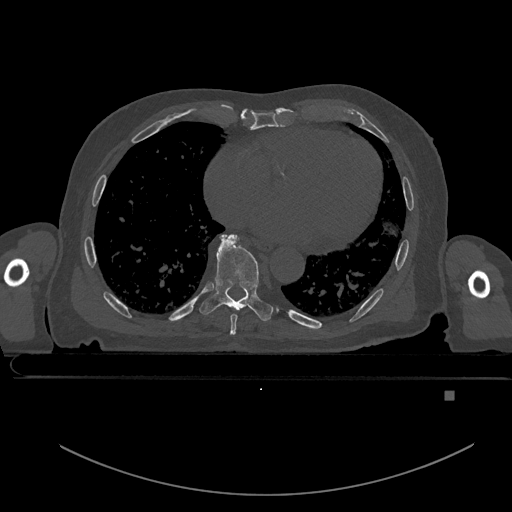
CT including the spine, one axial slice. Bone window (W 1800 / L 400 HU). 0.5 mm slice thickness. 512 × 512 image matrix, field of view 456 × 456 mm. Male patient, age 82 years. Case-level facts recorded for this patient, not image findings: primary cancer: prostate; vertebrae with lytic lesions (as recorded): T11, T9, T8, T2.
Outlined on this slice (semi-automatically segmented with operator editing):
- T7 vertebra: box from (x=228, y=235) to (x=238, y=334) px
- T8 vertebra: (x=199, y=234)–(x=273, y=321)